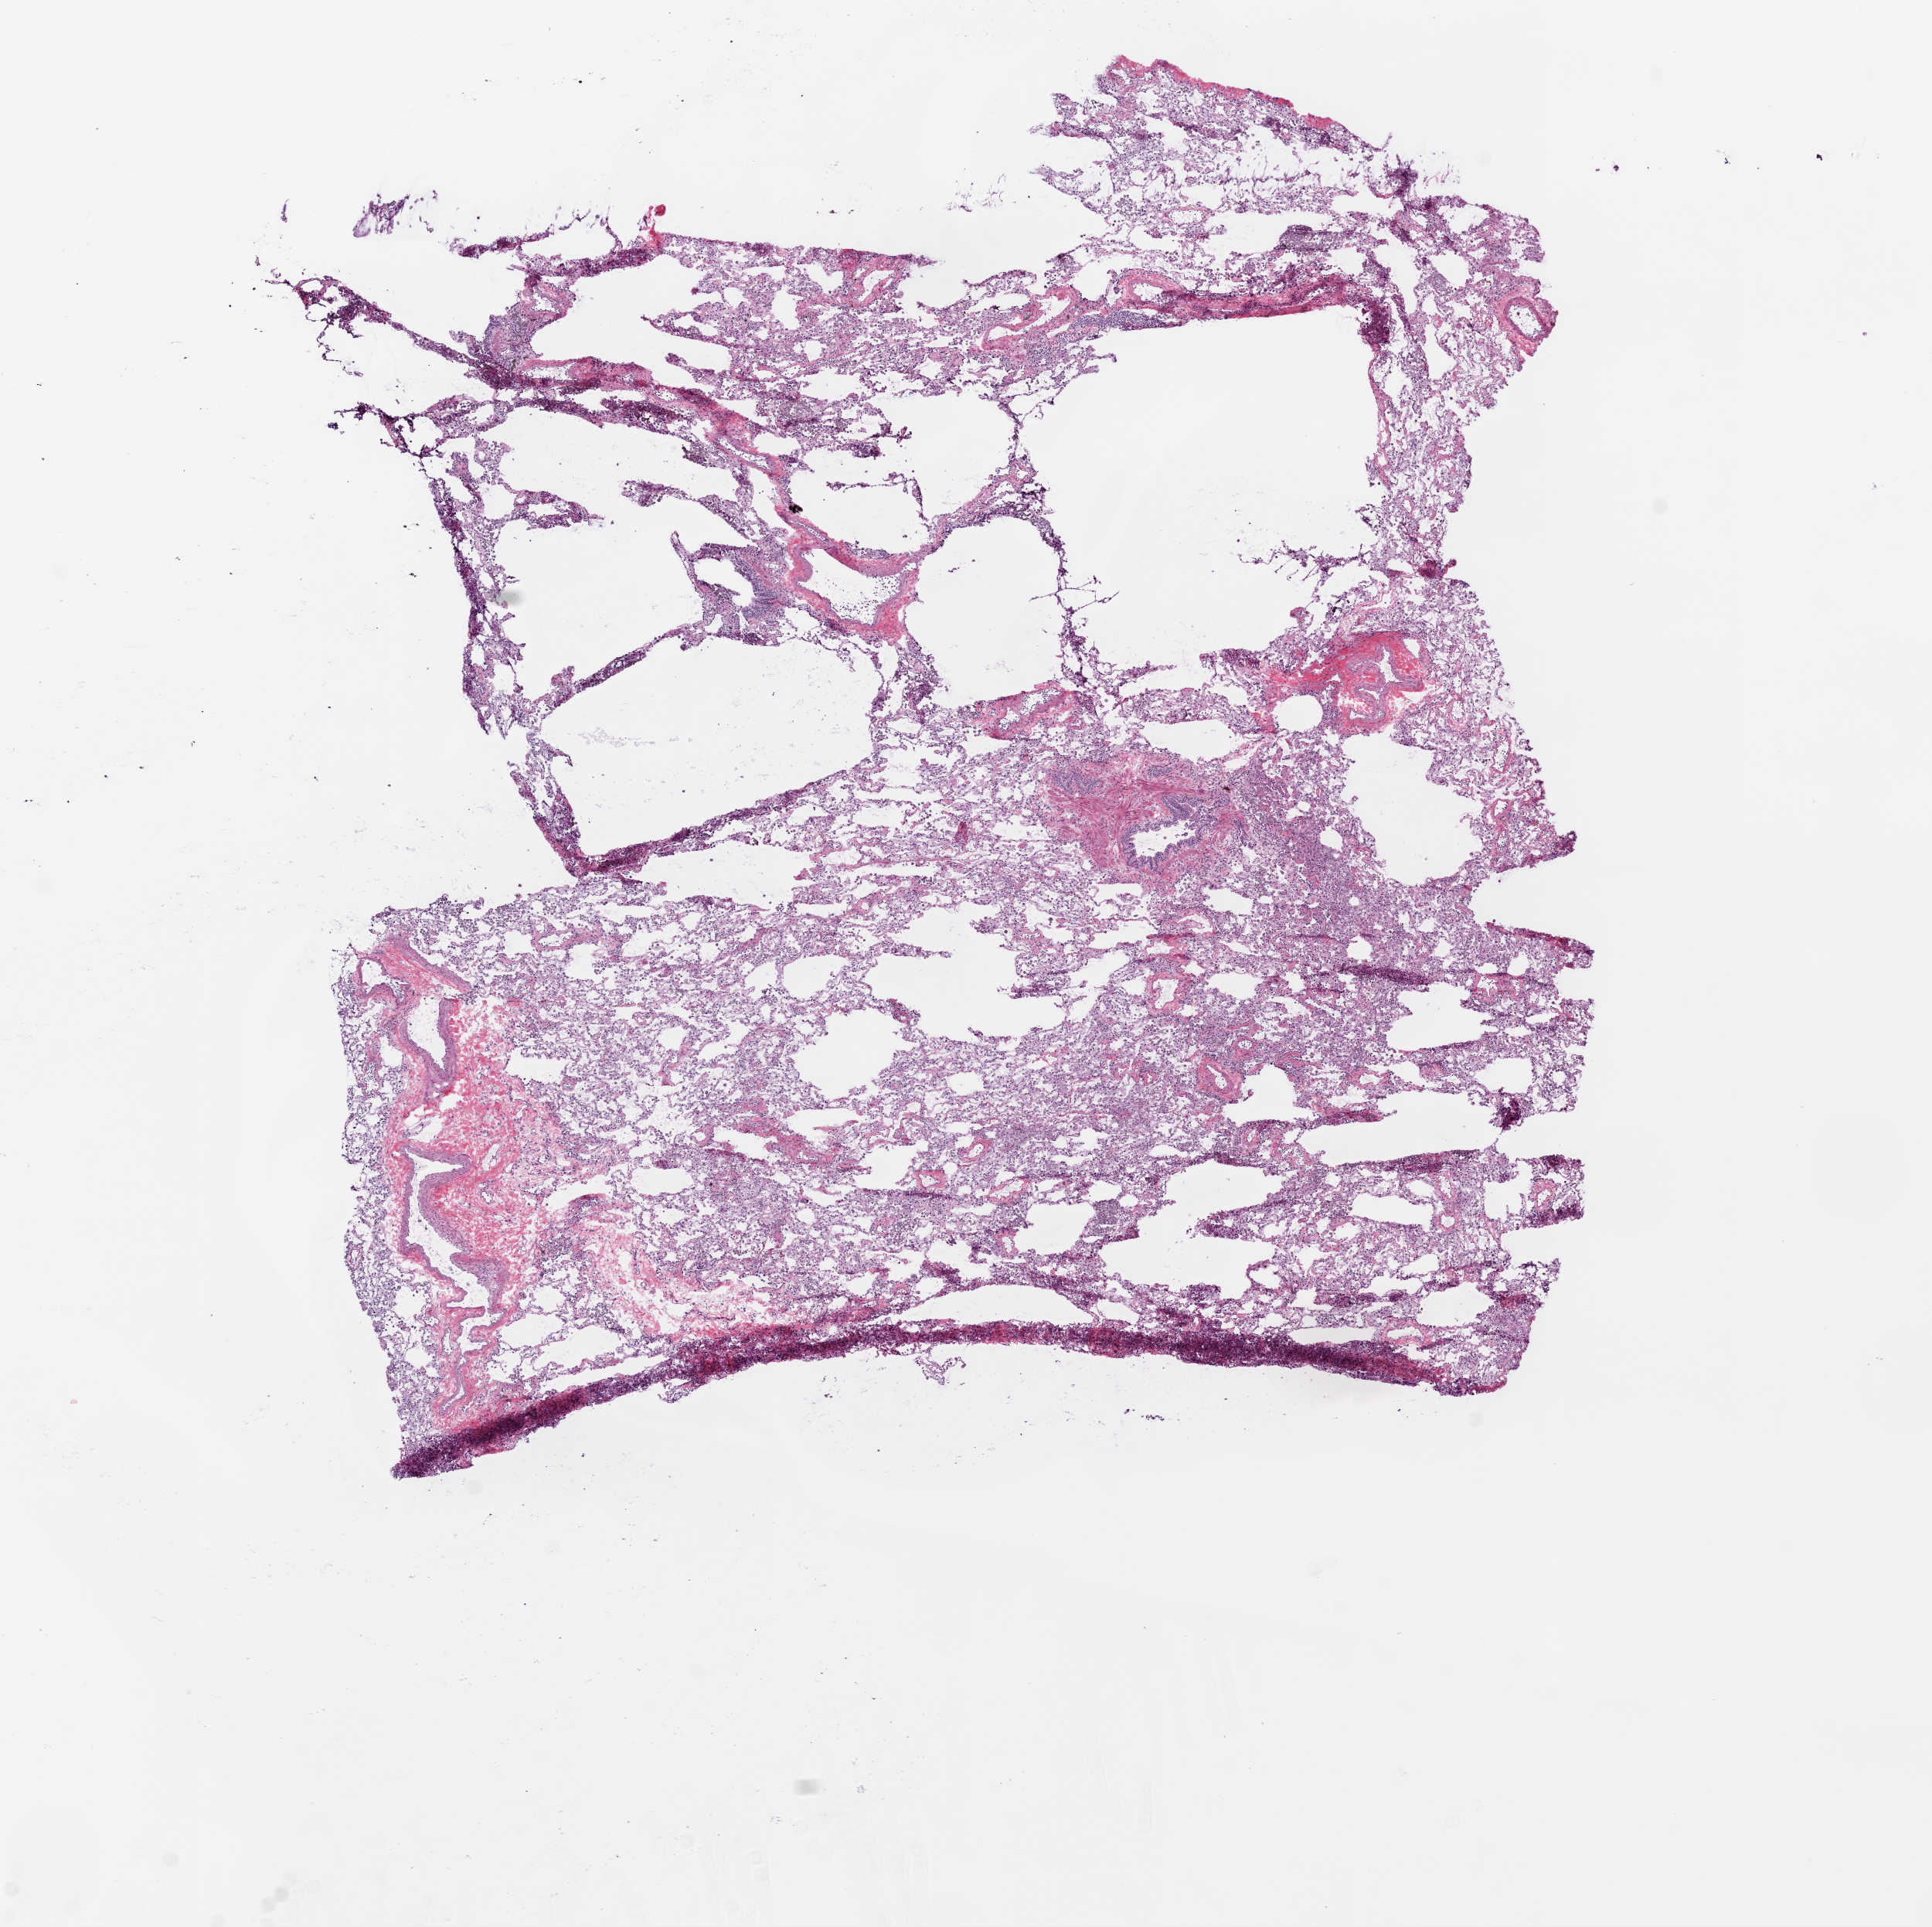
H&E-stained whole-slide image — low-resolution overview of the scanned area, about 10.0 x 10.0 mm (acquisition: 20x scan); frozen section; solid tissue normal (non-tumour tissue) sample from the lung. Female, age 33 years at initial diagnosis.
* this section: solid tissue normal sample (biorepository sample class)
* patient diagnosis: Adenocarcinoma, NOS (upper lobe, lung)